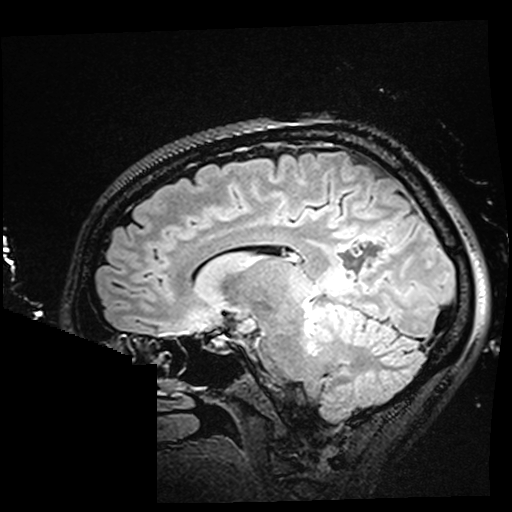
Brain MRI from a brain-tumour surgery series, one sagittal slice. Position 102 of 176 along the scan axis. T2 FLAIR. 1 mm slice thickness. 512 × 512 image matrix. From the clinical record (not read from this slice): histopathology: Oligodendroglioma; WHO grade: 2; IDH mutation: yes; tumour location: Right Parietal.
Structures marked on this image (manually delineated by an expert):
- residual tumour: bounding box <323,269,355,296> (left, top, right, bottom; pixels)